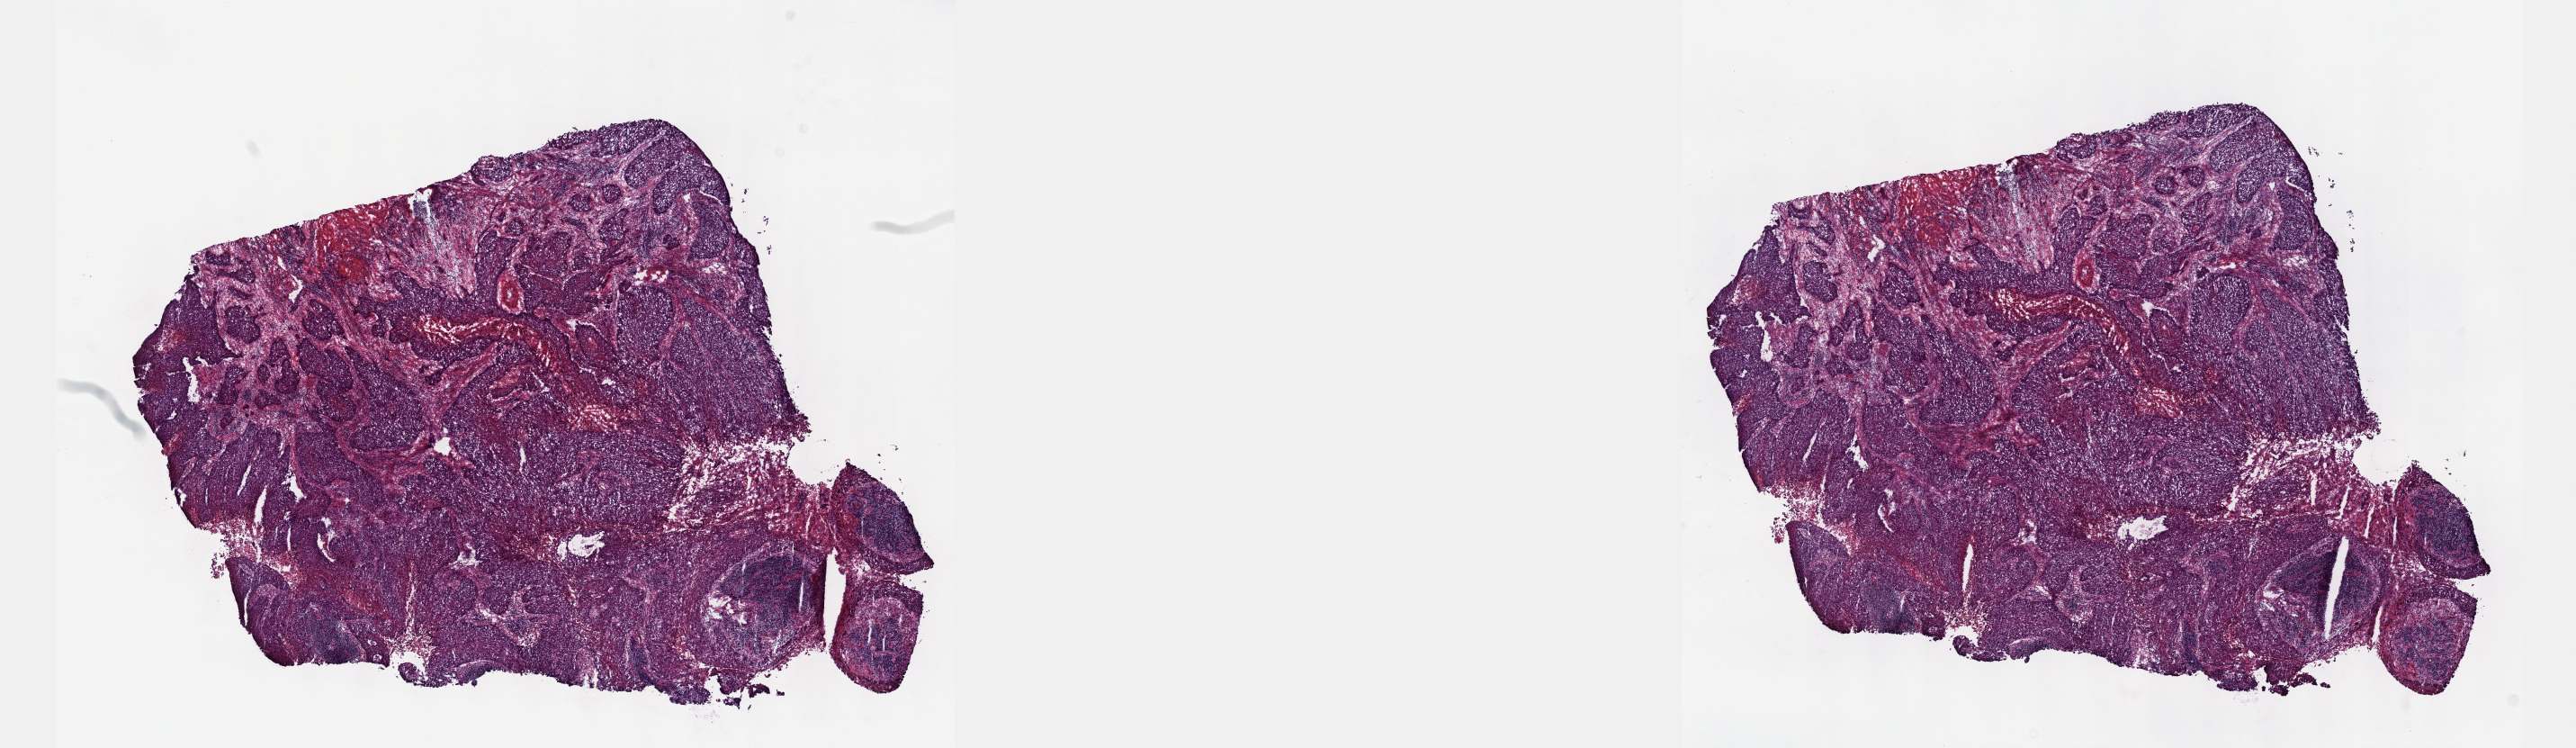
Digitized H&E tissue section (whole slide) — shown as a low-resolution overview of the whole scanned area (about 23.1 x 6.7 mm), frozen section, cervix, primary tumour sample. Patient: female, age at initial diagnosis 43 years. Slide review estimates, as recorded: tumour cells 60%, tumour nuclei 60%, normal cells 15%, stromal cells 15%, necrosis 10%. Infiltration values recorded for this section: lymphocyte infiltration 10%, monocyte infiltration 0%, neutrophil infiltration 2%.
Histologic diagnosis: Squamous cell carcinoma, keratinizing, NOS (cervix uteri). FIGO stage: IIB.